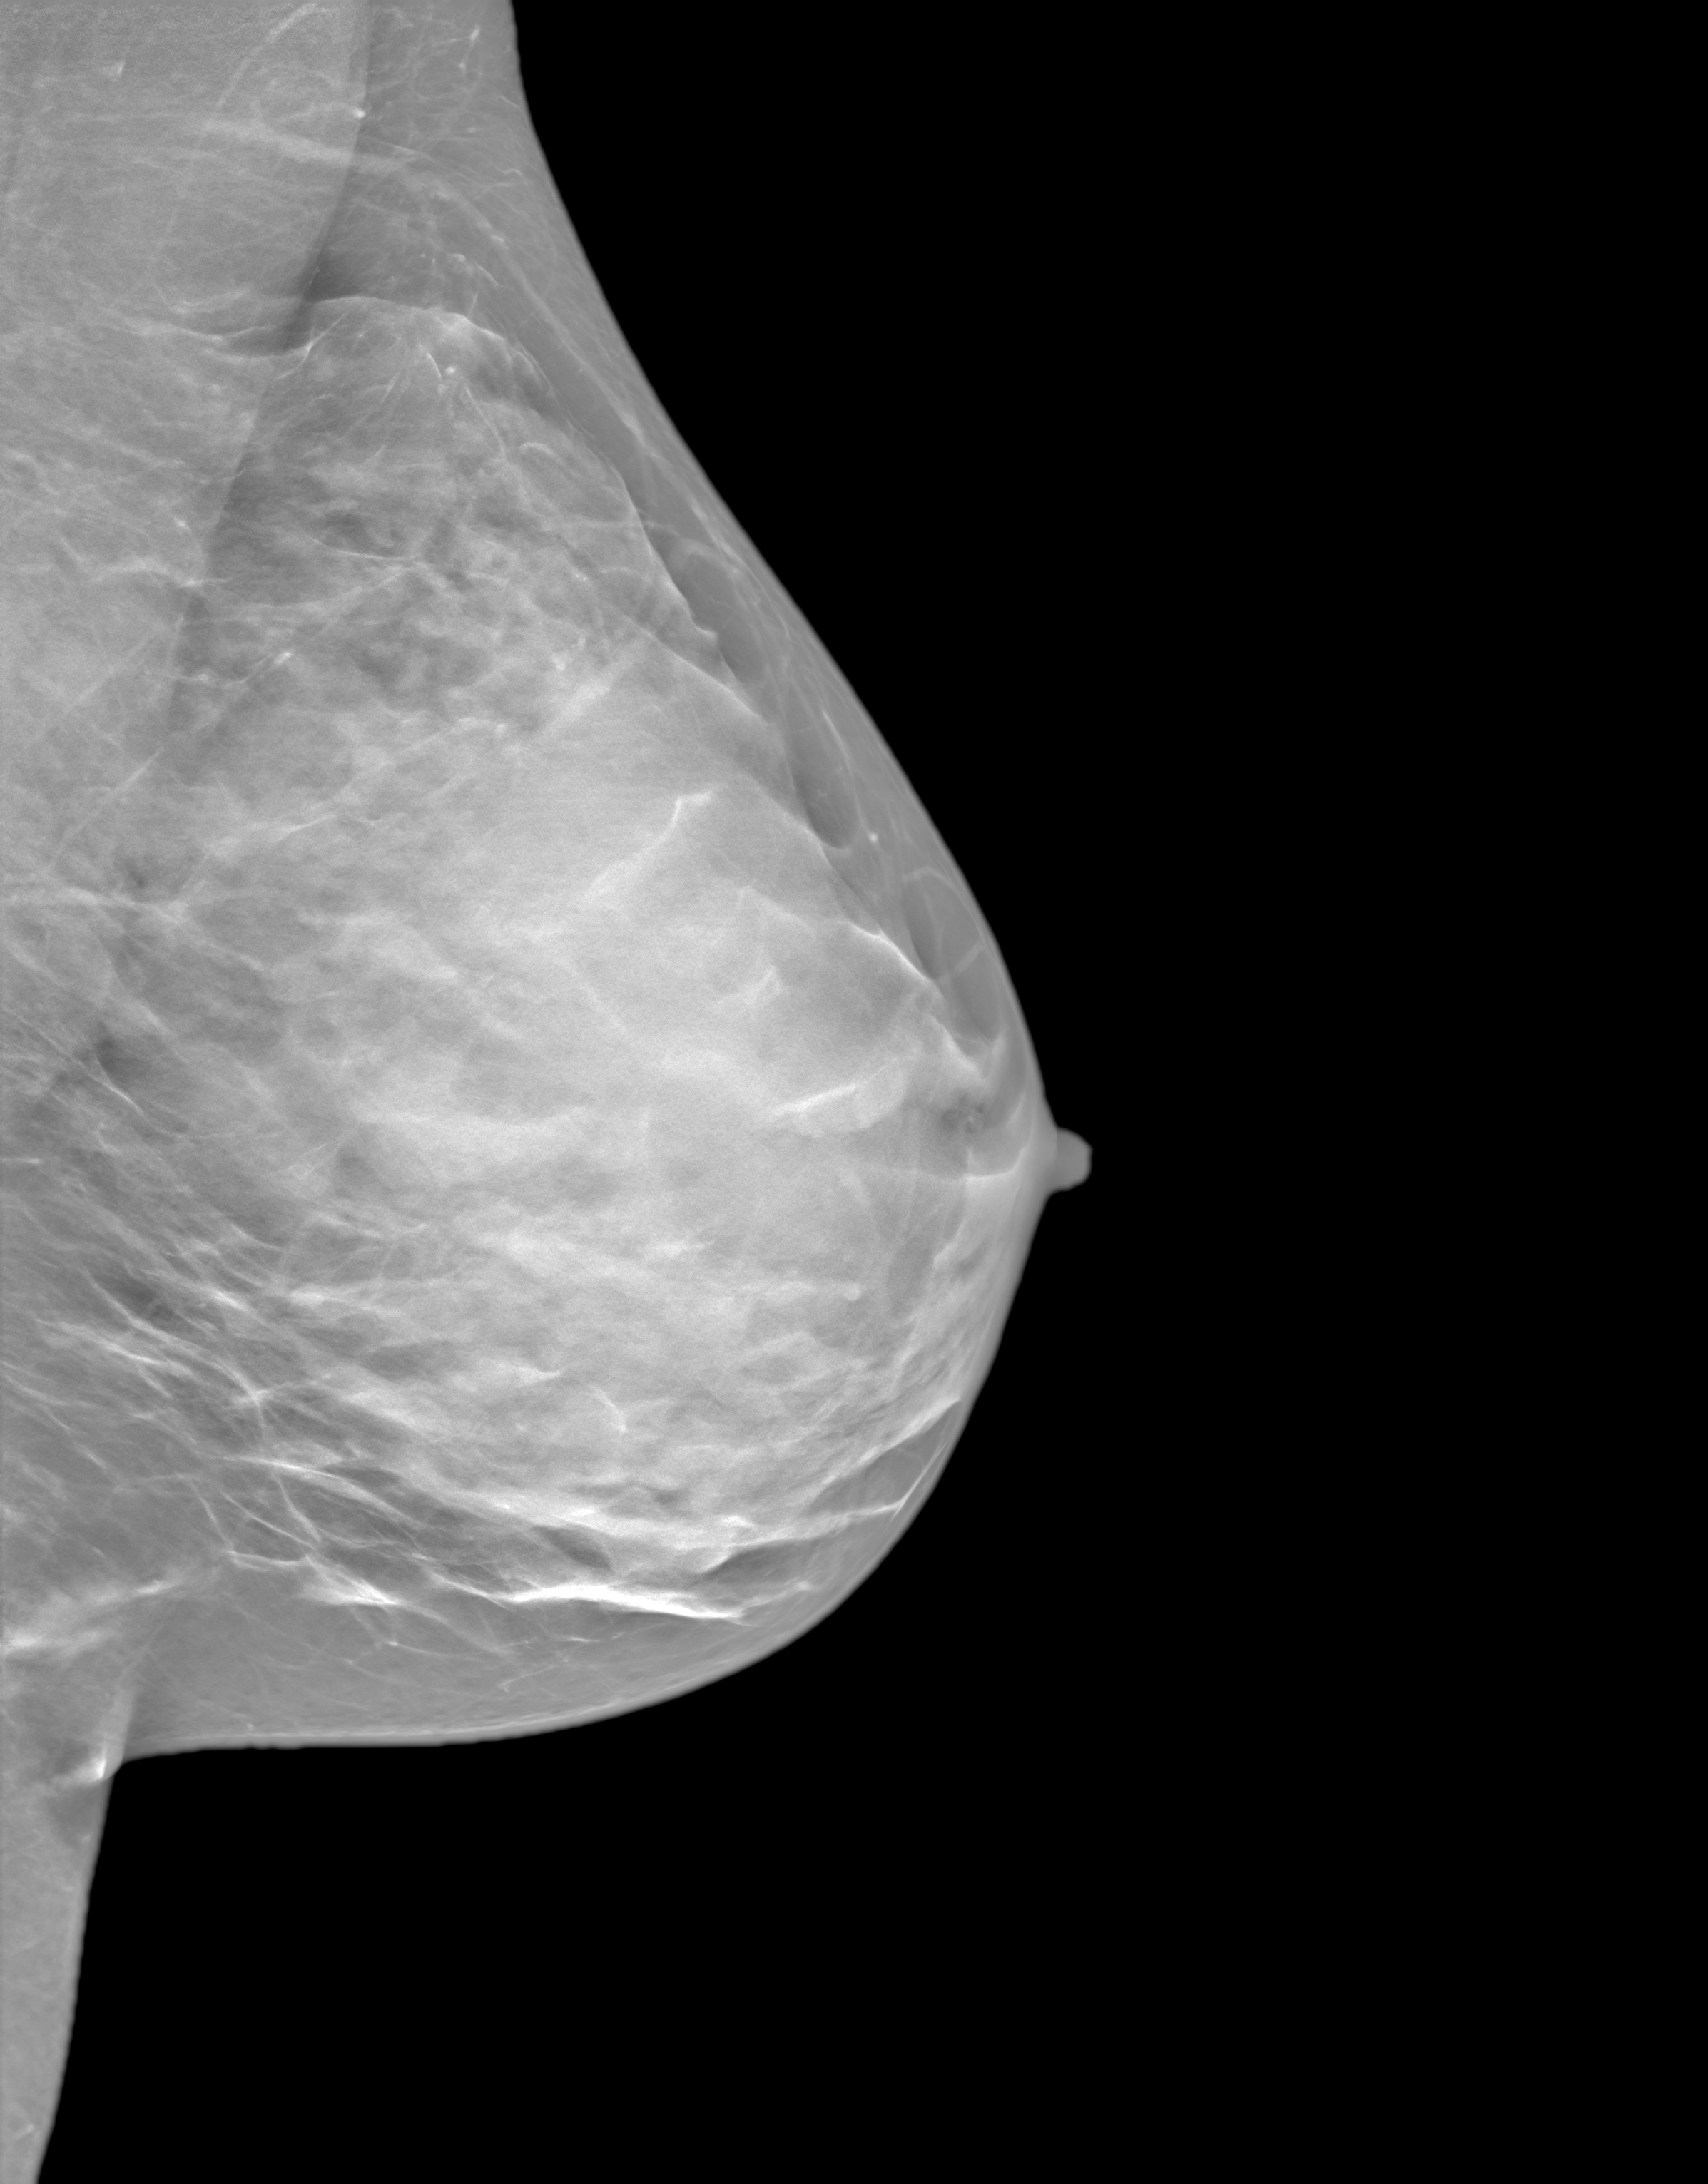
Synthetic 2-D view generated from a tomosynthesis acquisition (not an FFDM exposure), left breast, mediolateral oblique (MLO) view, annual screening mammography examination, system: SenoIris_1SP1.1(421). Female patient, age 43 years.
- BI-RADS breast density category at the screening exam (both breasts, scale 1–4): 4
- final BI-RADS category for the screening round (tomosynthesis exam, both breasts): category 1
- recall: no recall after this screen